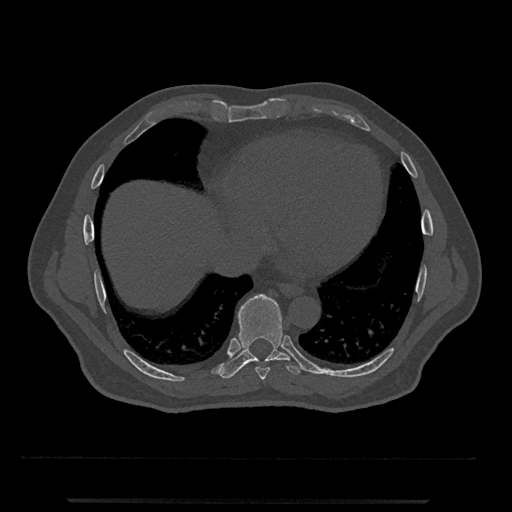
CT including the spine, one axial slice. Slice 592 of 797 in the series (ordered by position). Reconstruction kernel Br40s/3. 120 kVp. Bone window (W 1800 / L 400 HU). 0.5 mm slice thickness. 512 × 512 image matrix, field of view 419 × 419 mm. Patient: male, 63 years. From the clinical record (not read from this slice): primary cancer: prostate.
Outlined on this slice (semi-automatic segmentation, software-assisted and operator-edited):
- T8 vertebra: bounding box [x1, y1, x2, y2] px = [255, 366, 270, 380]
- T9 vertebra: [220, 294, 303, 379]